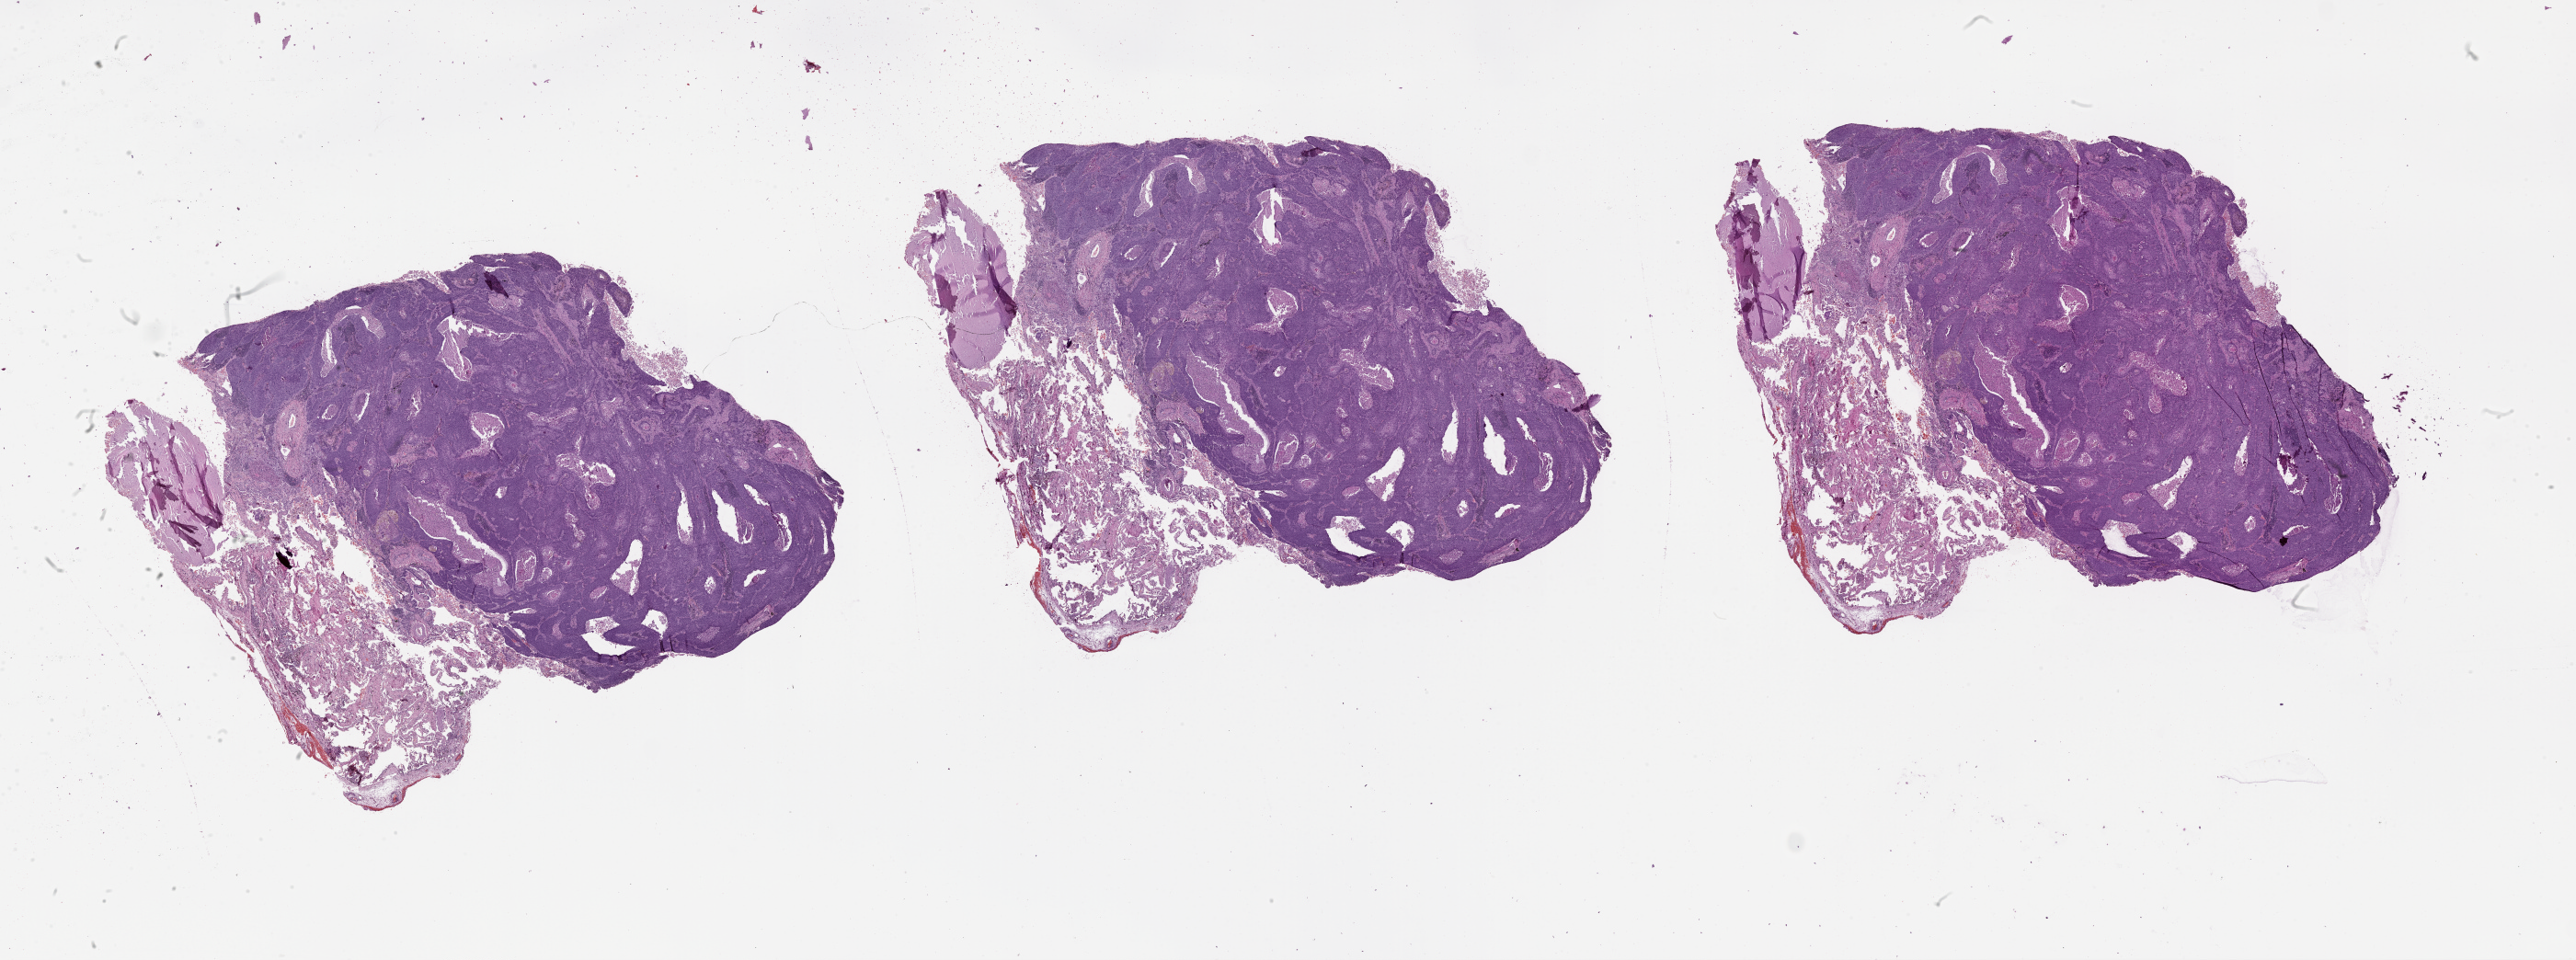
Whole-slide histology image, H&E, low-resolution overview of the scanned area, about 45.1 x 16.8 mm (acquisition: 20x scan); lung, tumour tissue. Patient: male, age 67 years.
Patient diagnosis (cohort enrolment): squamous cell carcinoma (lung).